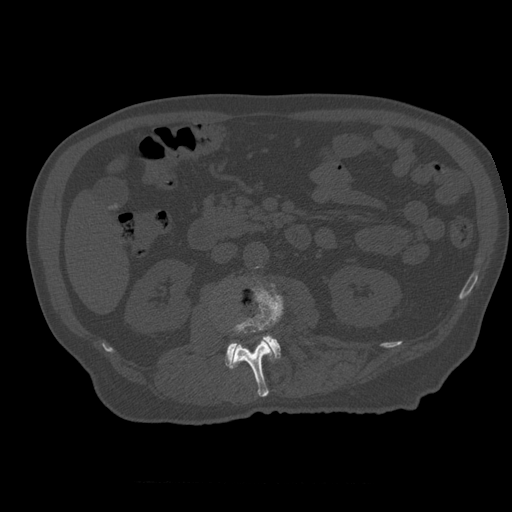
CT including the spine, one axial slice; position 205 of 399 along the scan axis; 120 kVp; bone window (W 1800 / L 400 HU); 1.25 mm slice thickness; 512 × 512 image matrix. Patient age 73 years. Case-level facts recorded for this patient, not image findings: primary cancer: prostate.
Outlined on this slice (semi-automatically segmented with operator editing):
- L2 vertebra: bounding box <228,285,283,397> (left, top, right, bottom; pixels)
- L3 vertebra: <225,336,281,369>